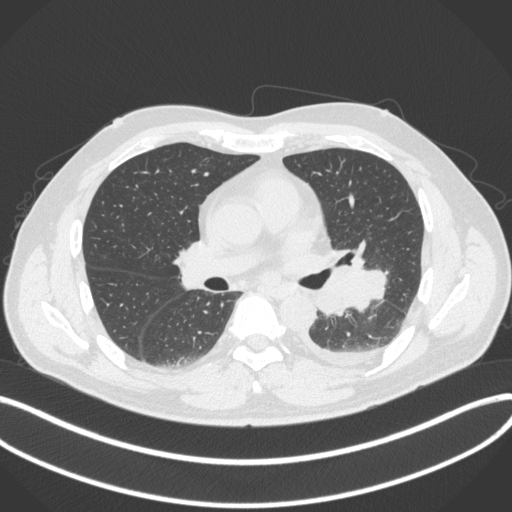
Chest CT, one axial slice. Position 198 of 350 along the scan axis. Reconstruction kernel B31f. 120 kVp. Lung window (W 1500 / L -600 HU). 512 × 512 image matrix, field of view 400 × 400 mm. Male patient, age 58 years. From the clinical record (not read from this slice): clinical TNM (as recorded): T3 N1 M1b; histopathological grade: G3.
Annotated regions visible in this slice (bounding box drawn by a radiologist):
- lung tumour (recorded histology: small cell carcinoma): bounding box [x1, y1, x2, y2] px = [313, 261, 390, 318]